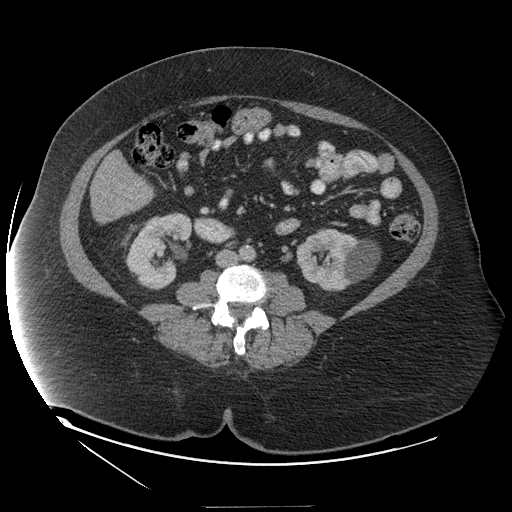
Contrast-enhanced abdominal CT (liver protocol), one axial slice; position 28 of 127 along the scan axis; 140 kVp; soft-tissue window (W 400 / L 40 HU); 512 × 512 image matrix, field of view 480 × 480 mm. From the clinical record (not read from this slice): diagnosis: hepatocellular carcinoma (patient treated with transarterial chemoembolisation; whether this scan precedes or follows treatment is not stated here); TNM stage (as recorded): Stage-II; Child-Pugh class: A; tumour differentiation: well differentiated.
Annotated regions visible in this slice (semi-automatic segmentation, software-assisted and operator-edited):
- liver parenchyma outside the tumour (the mass and vessels are separate outlines, so this box may not span the whole liver): bounding box <92,192,134,222> (left, top, right, bottom; pixels)